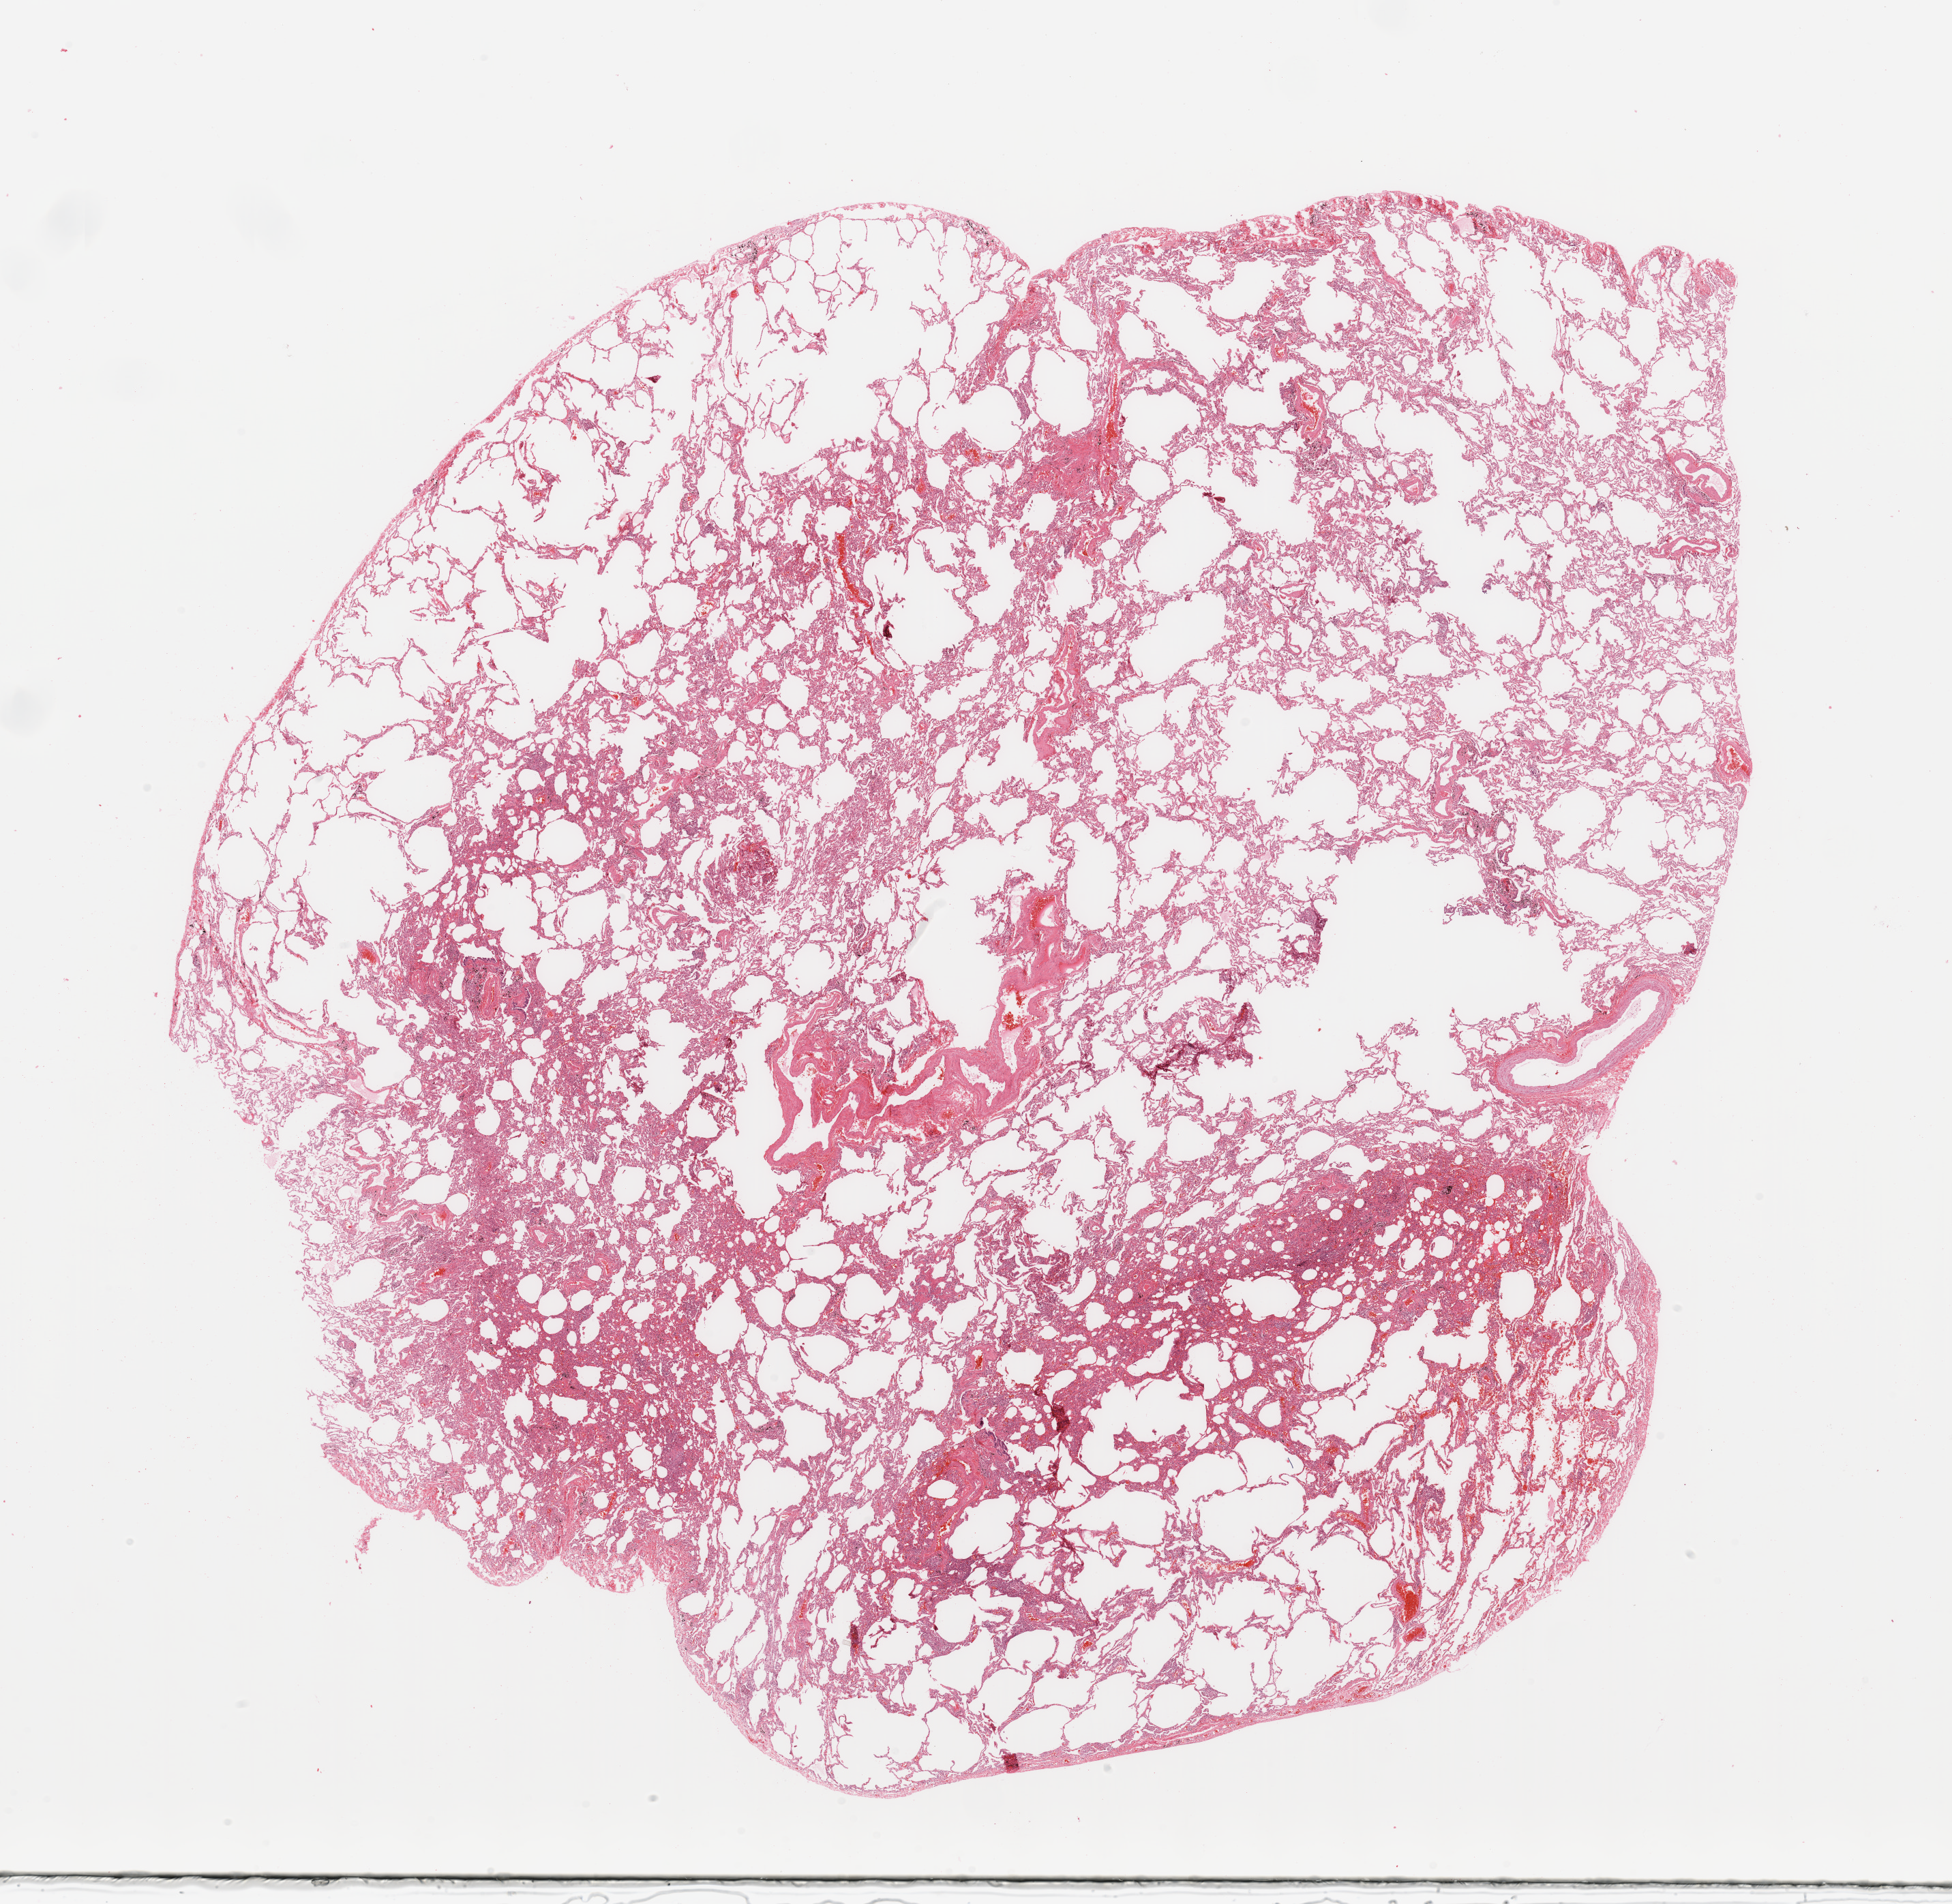
Whole-slide histology image, H&E-stained, low-resolution overview of the scanned area, about 22.6 x 22.1 mm (acquisition: 20x scan), normal (non-tumour) tissue sample, sampled site: lung. Female, 66 y/o.
This section: normal (non-tumour) tissue from the same patient. Patient diagnosis: Adenocarcinoma, NOS.